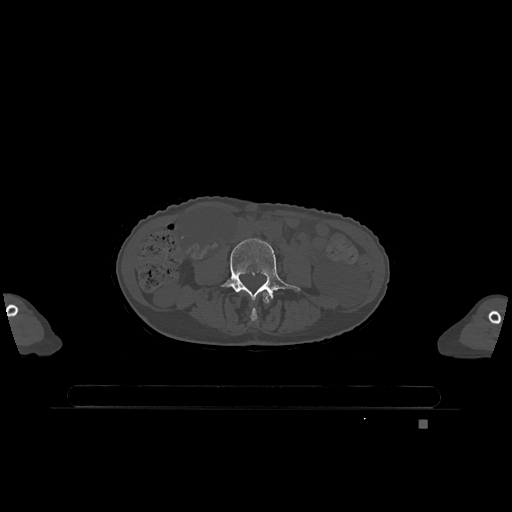
CT including the spine, one axial slice. Slice 305 of 1317 in the series (ordered by position). Bone window (W 1800 / L 400 HU). 0.5 mm slice thickness. 512 × 512 image matrix, field of view 500 × 500 mm. Patient: female, 74 years. From the clinical record (not read from this slice): primary cancer: lung.
Structures marked on this image (semi-automatic segmentation, software-assisted and operator-edited):
- L3 vertebra: box from (x=241, y=290) to (x=271, y=321) px
- L4 vertebra: (x=221, y=238)–(x=301, y=300)